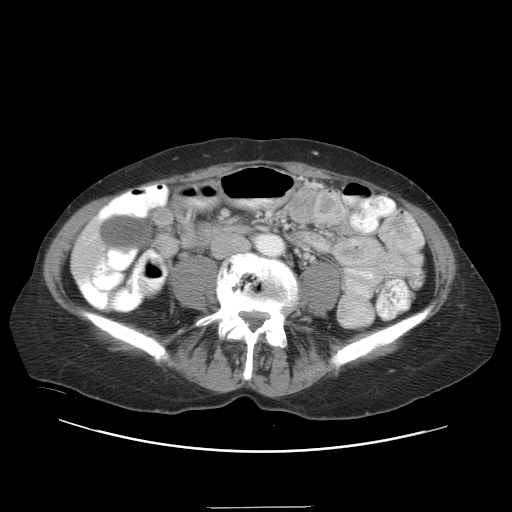
Contrast-enhanced abdominal CT, one axial slice; slice 2 of 38 in the series (ordered by position); 120 kVp; soft-tissue window (W 400 / L 40 HU); 5 mm slice thickness; 512 × 512 image matrix. Female patient, age 64 years. From the clinical record (not read from this slice): diagnosis: colorectal cancer liver metastases, imaged before liver resection; multiple liver metastases: no; largest metastasis: 3.8 cm; disease in both lobes: yes.
Annotated regions visible in this slice (outlined manually by an expert reader):
- liver: box from (x=74, y=225) to (x=101, y=273) px